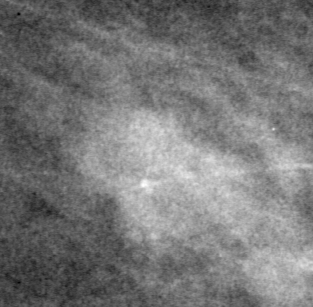
Crop from a digitized film mammogram around one marked abnormality; right breast; MLO view; BI-RADS breast density category 3 (scale 1–4).
Marked abnormality: mass, shape lobulated, margins ill defined; BI-RADS assessment category 4; pathology (as recorded): malignant.